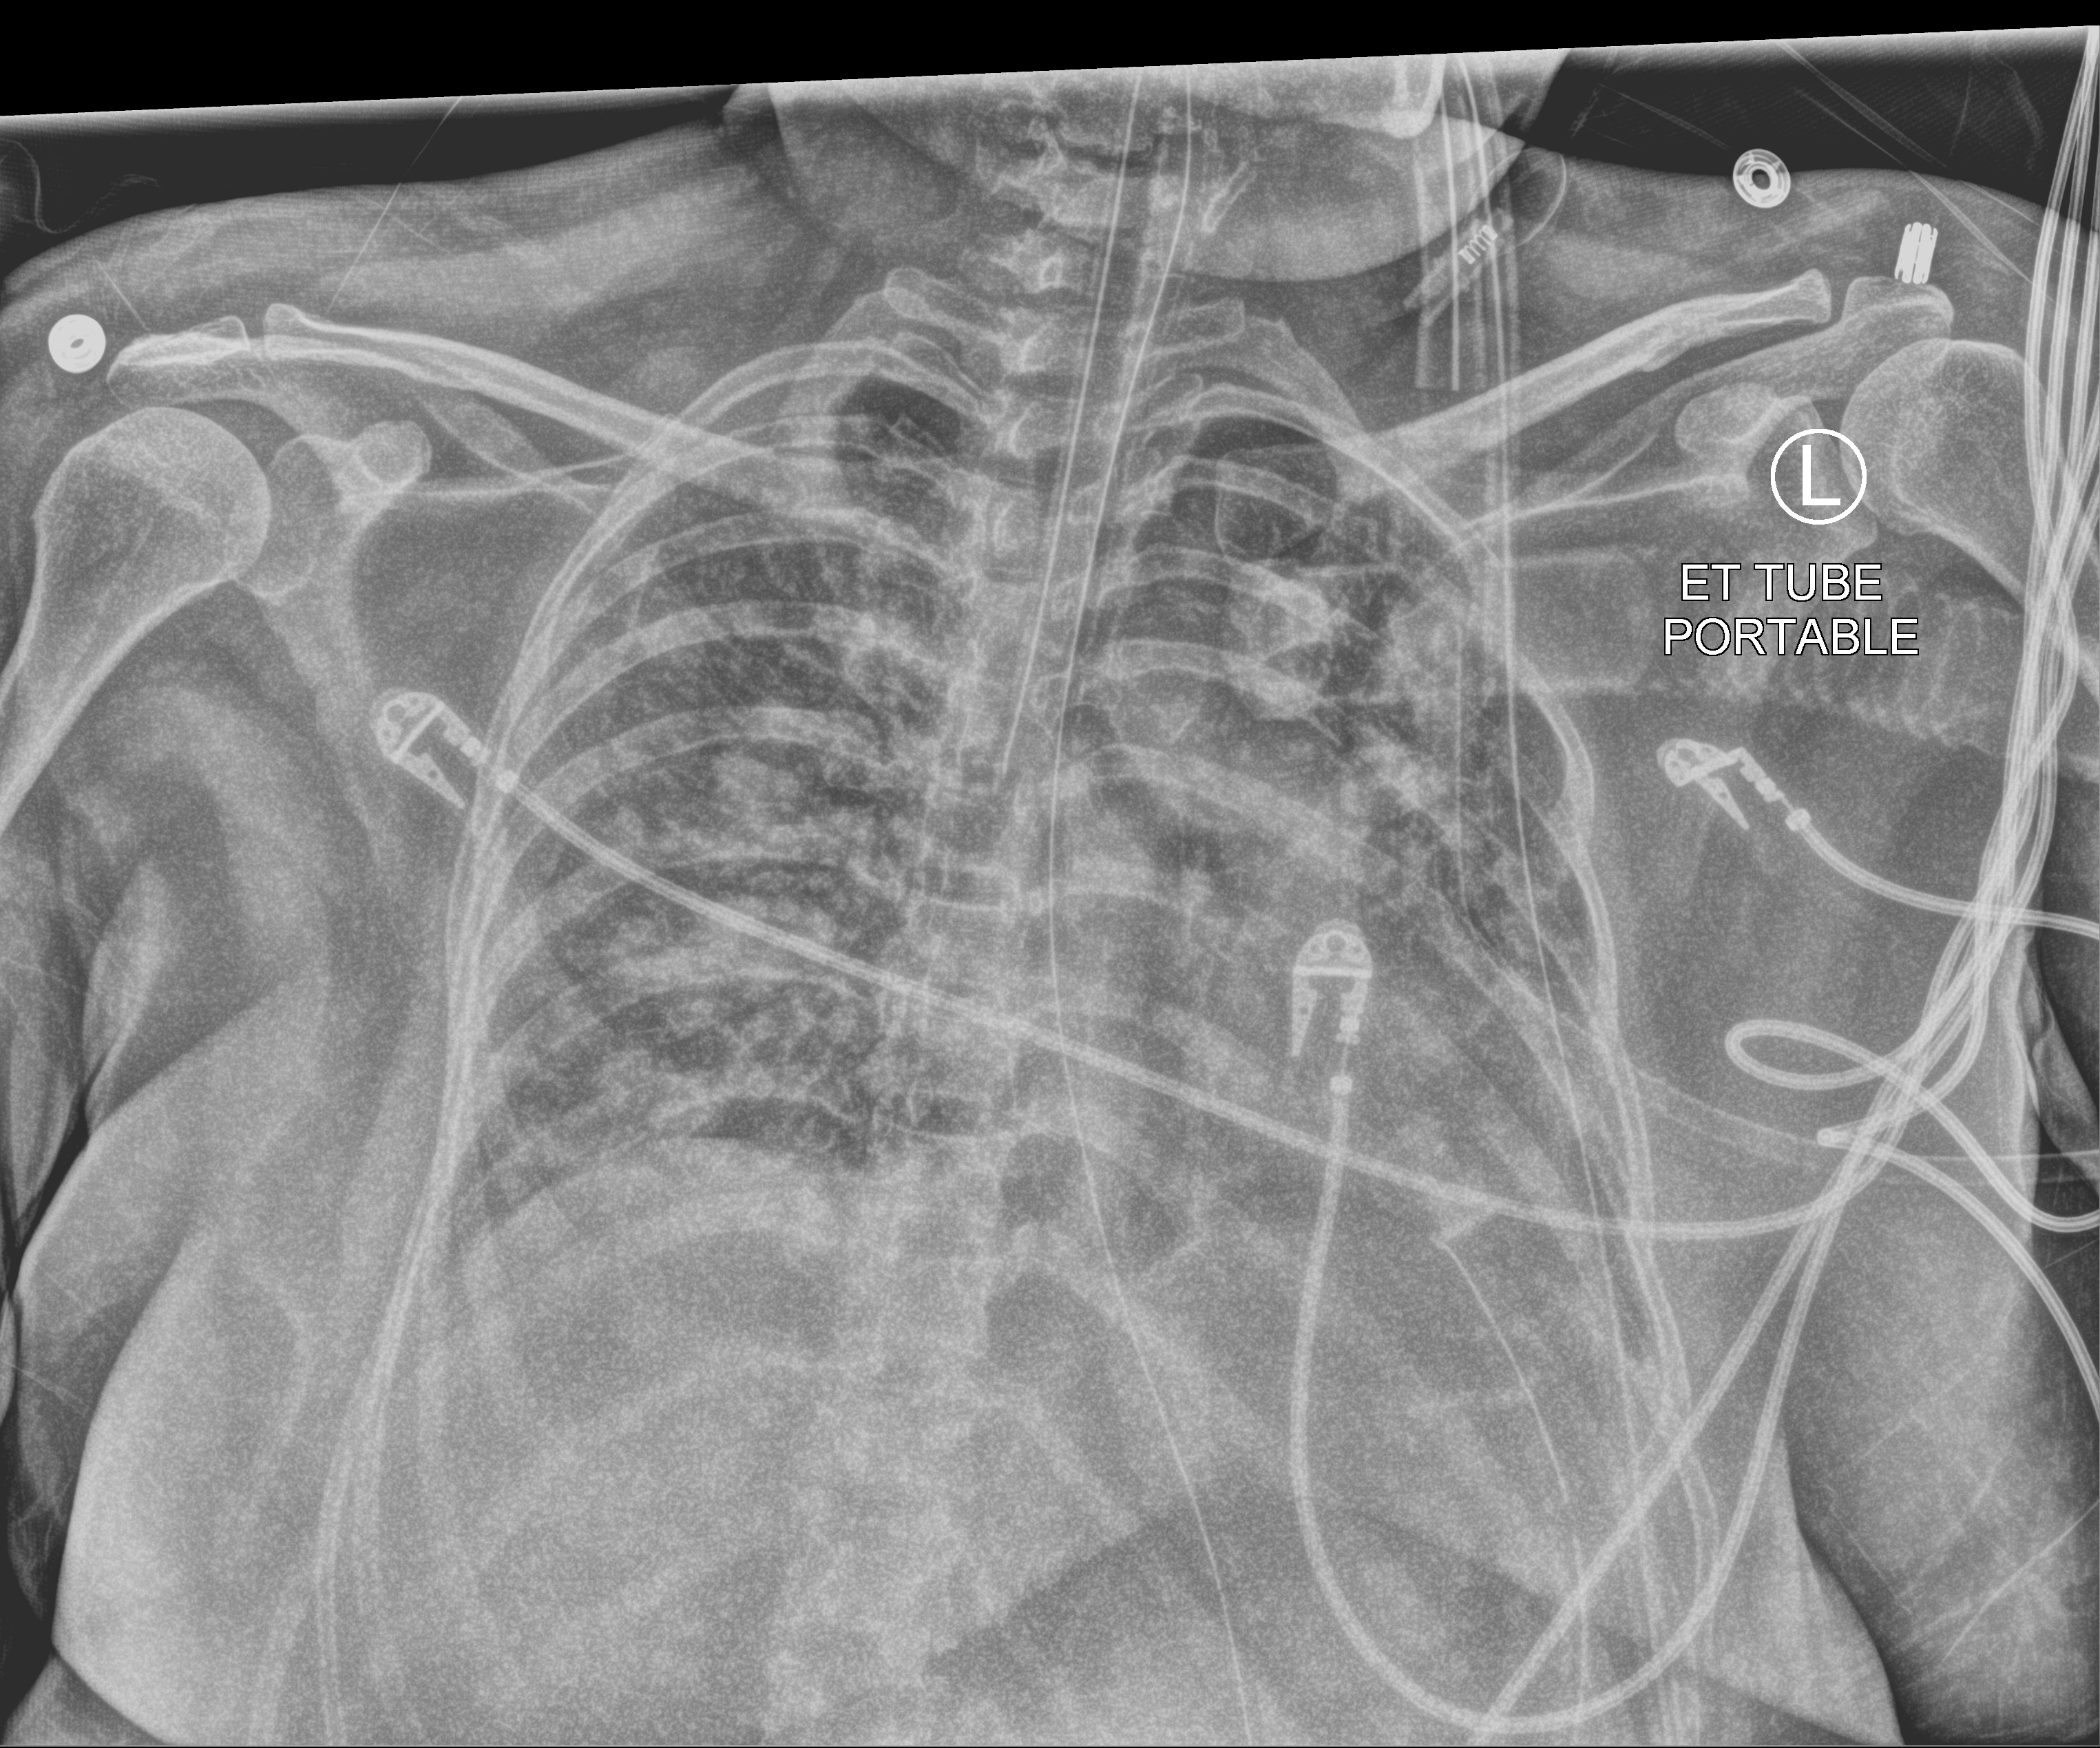
Portable chest radiograph, anteroposterior (AP) projection. Patient hospitalised with COVID-19, aged 18–59 years.
Admission-level facts for this patient (not findings on this image; timing relative to this image not recorded):
- hypertension (admission record): no